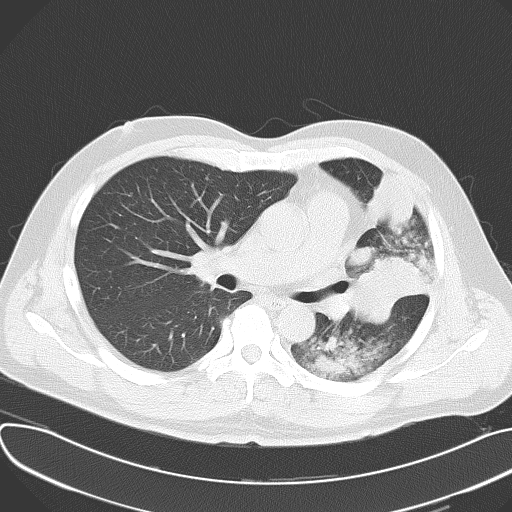
Chest CT, one axial slice; position 37 of 62 along the scan axis; reconstruction kernel B70f; lung window (W 1500 / L -600 HU); 5 mm slice thickness; 512 × 512 image matrix. Male patient, age 48 years. Case-level facts recorded for this patient, not image findings: clinical TNM (as recorded): T4 N0 M0.
Outlined on this slice (bounding box drawn by a radiologist):
- lung tumour (recorded histology: adenocarcinoma): bounding box [x1, y1, x2, y2] px = [348, 242, 429, 327]